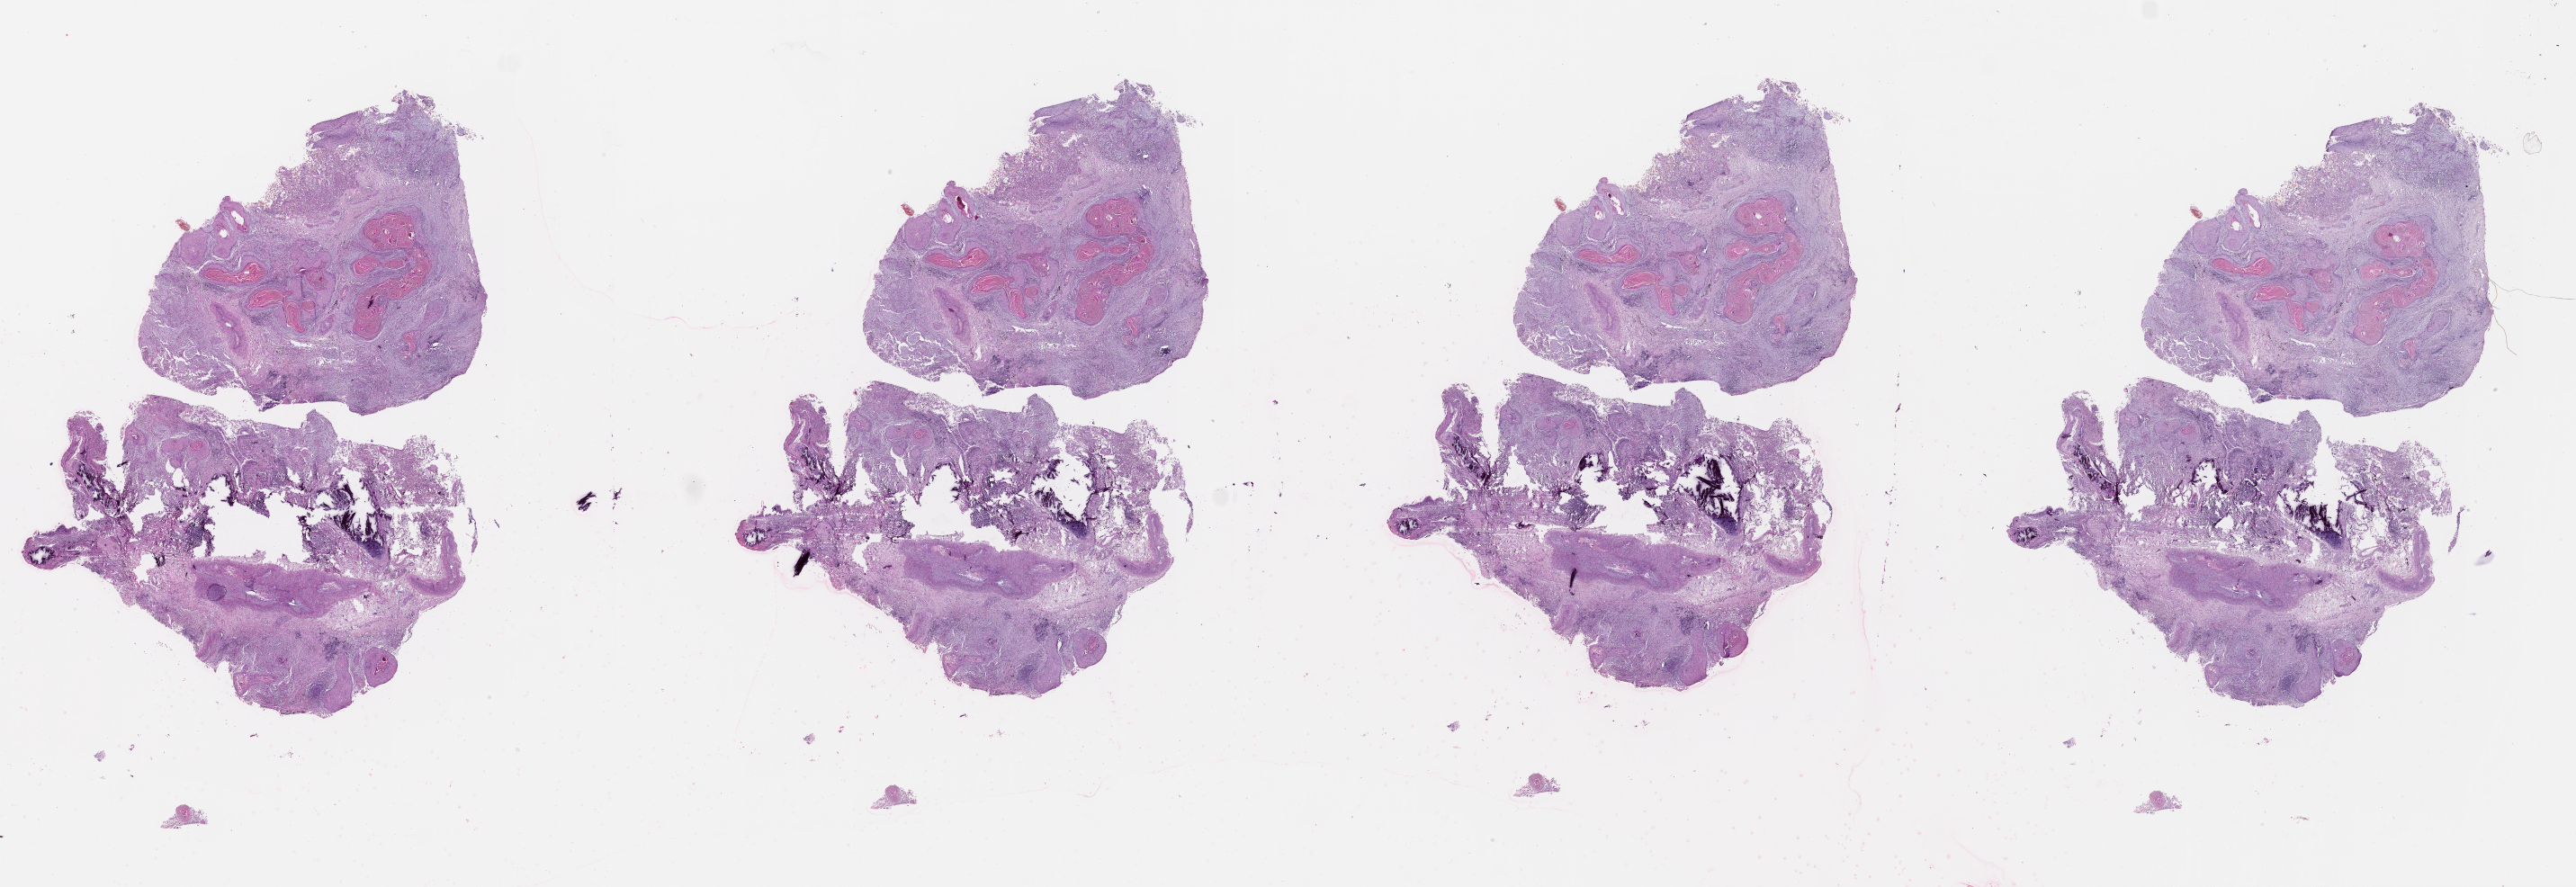
Digitized H&E tissue section (whole slide), shown as a low-resolution overview of the whole scanned area (about 46.1 x 15.9 mm, slide scanned at 20x); lung, tumour tissue. Patient: male, age 72 years.
Patient diagnosis (cohort enrolment): squamous cell carcinoma (lung).